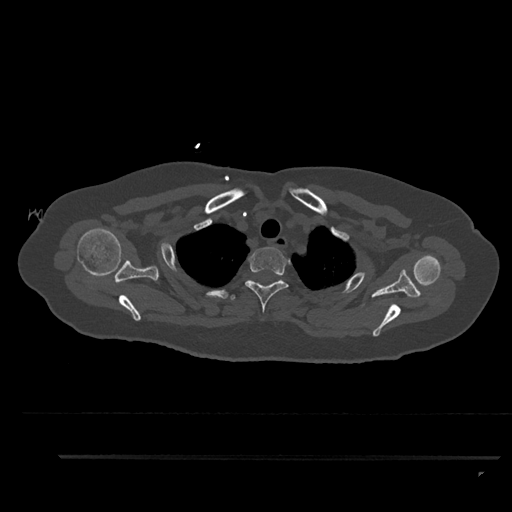
CT including the spine, one axial slice; position 719 of 797 along the scan axis; reconstruction kernel Br40s/3; bone window (W 1800 / L 400 HU); 0.5 mm slice thickness; 512 × 512 image matrix, field of view 408 × 408 mm. Female patient, age 44 years. Case-level facts recorded for this patient, not image findings: primary cancer: renal; vertebrae with lytic lesions (as recorded): L1.
Outlined on this slice (semi-automatic segmentation, software-assisted and operator-edited):
- T2 vertebra: bounding box [x1, y1, x2, y2] px = [245, 247, 289, 313]
- T3 vertebra: [230, 295, 235, 300]